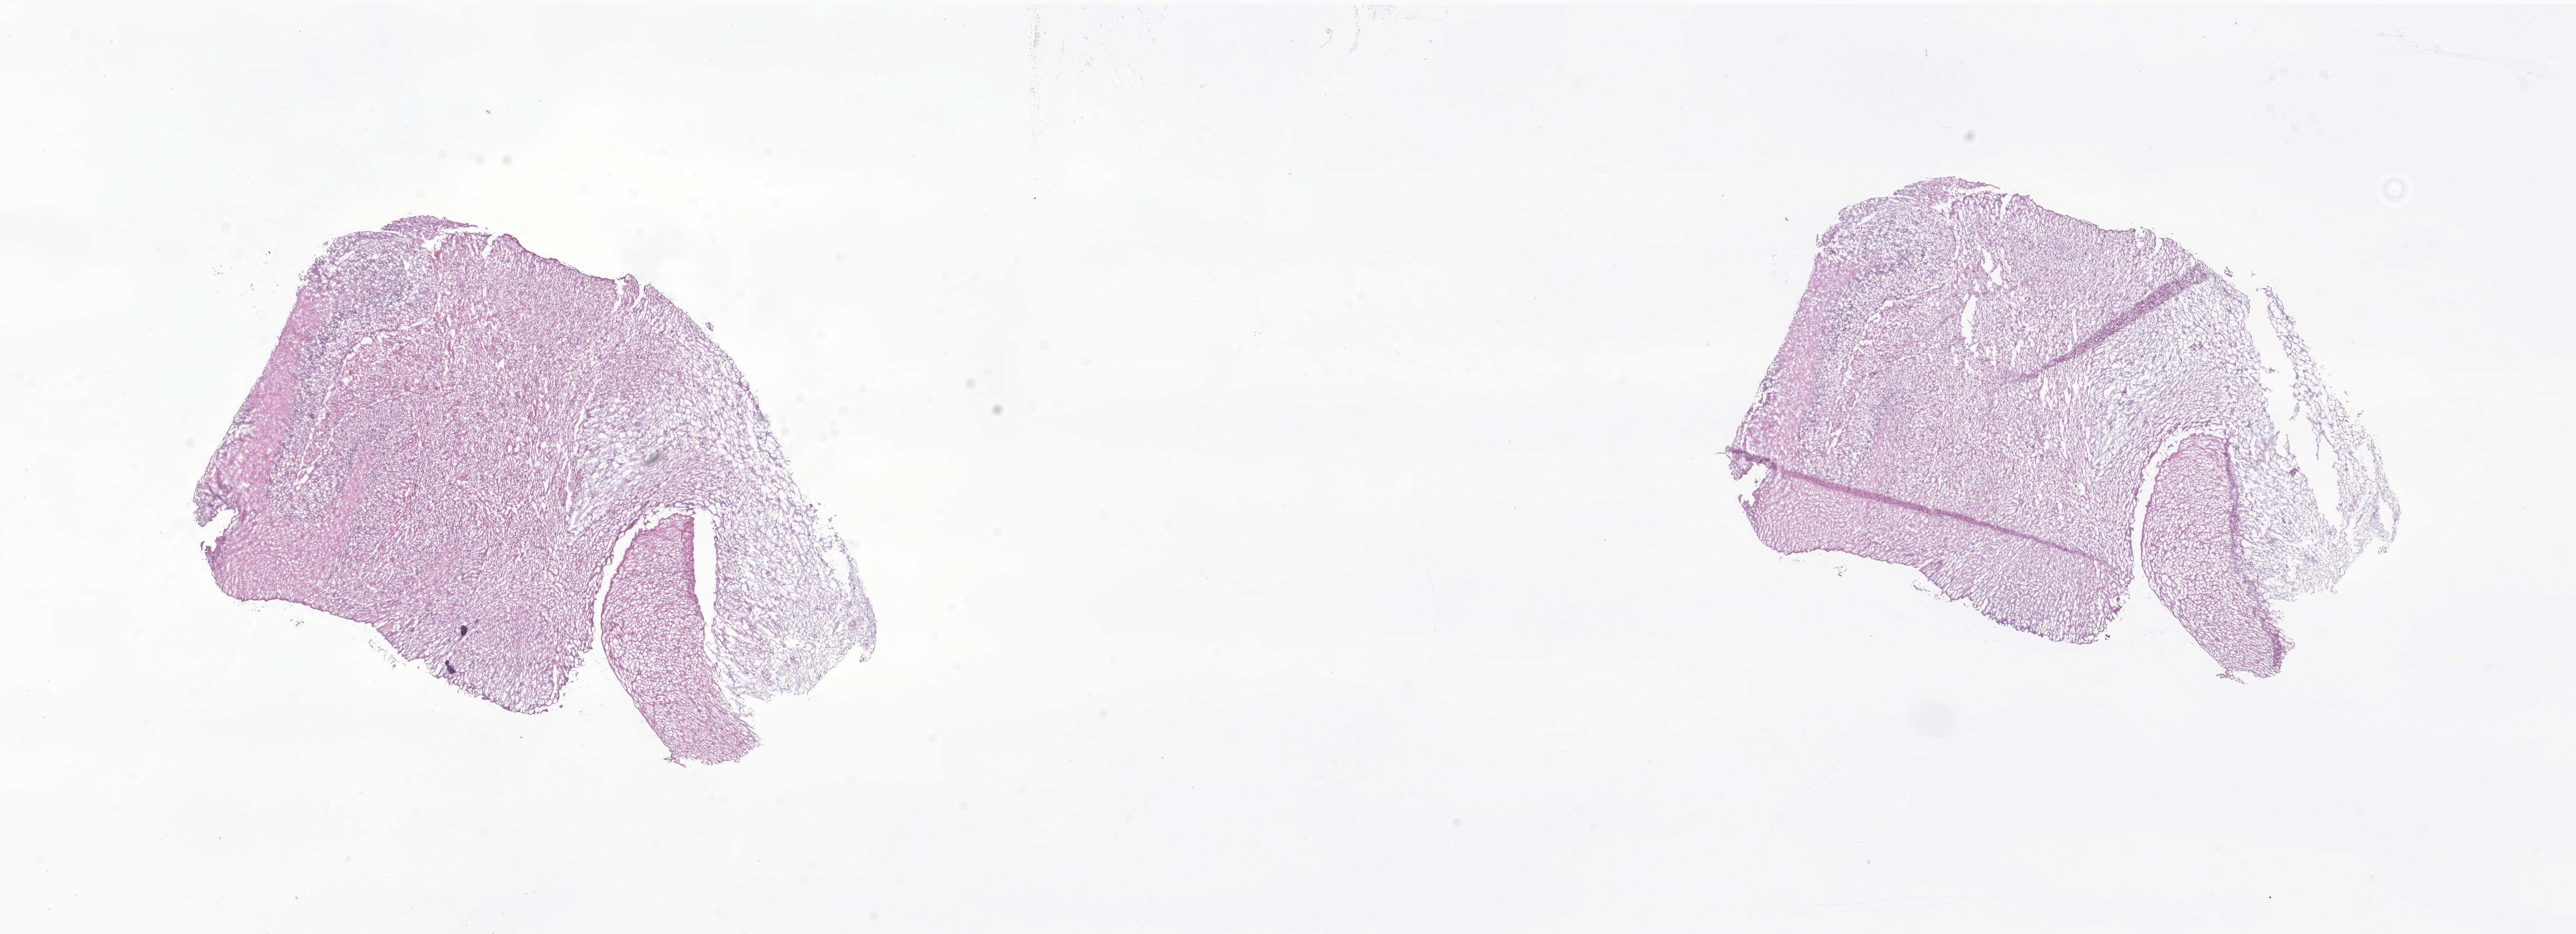
Haematoxylin and eosin whole-slide image of tumor tissue from the cerebellum — low-resolution overview of the scanned area, about 28.9 x 10.5 mm; frozen section. Patient: male, age 161 months (13 years 5 months).
- recorded diagnosis: Pilocytic astrocytoma